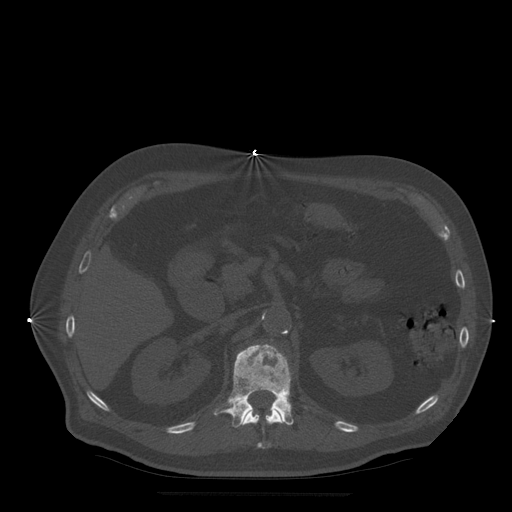
CT including the spine, one axial slice; position 203 of 522 along the scan axis; bone window (W 1800 / L 400 HU); 1.25 mm slice thickness; 512 × 512 image matrix. Patient age 72 years. Case-level facts recorded for this patient, not image findings: primary cancer: prostate.
Structures marked on this image (semi-automatically segmented with operator editing):
- L1 vertebra: box from (x=214, y=345) to (x=294, y=428) px
- T12 vertebra: (x=243, y=408)–(x=283, y=449)